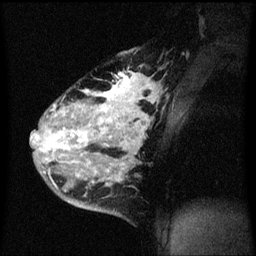
Breast MRI (dynamic contrast-enhanced), one sagittal slice. Position 44 of 60 along the scan axis. Dynamic contrast-enhanced series, image 2 of 3 at this slice position (ordered by acquisition). 1.5 T. TE 4.2 ms, TR 8.4 ms. 2 mm slice thickness. 256 × 256 image matrix. Female patient, age 34 years. Case-level facts recorded for this patient, not image findings: setting: breast cancer imaged before/during neoadjuvant chemotherapy; receptor status: HR-positive, HER2-negative.
Annotated regions visible in this slice (semi-automatically segmented with operator editing):
- analysis volume of interest (the breast-tissue region the enhancement analysis was run in; not a lesion): bounding box <34,48,157,215> (left, top, right, bottom; pixels)
- tumour enhancement mask (voxels above the 70 % enhancement threshold inside the analysis volume of interest): <34,72,155,185>